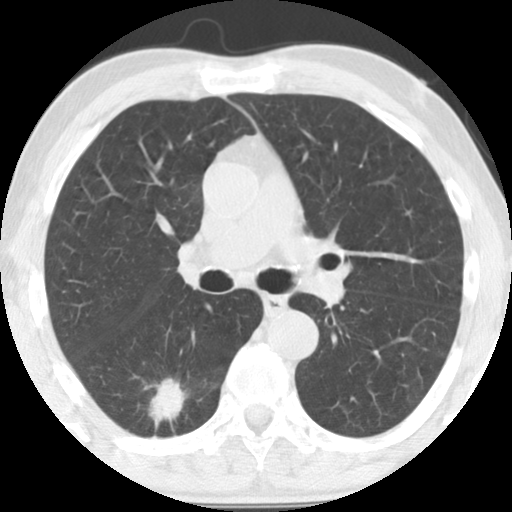
Low-dose screening chest CT, one axial slice; position 86 of 135 along the scan axis; reconstruction kernel STANDARD; 120 kVp; lung window (W 1500 / L -600 HU); 2.5 mm slice thickness; 512 × 512 image matrix, field of view 300 × 300 mm.
Annotated regions visible in this slice (expert manual segmentation):
- lesion 1 (tumor, lower lobe of right lung): bounding box (x1, y1, x2, y2) in pixels: (149, 378, 186, 421)